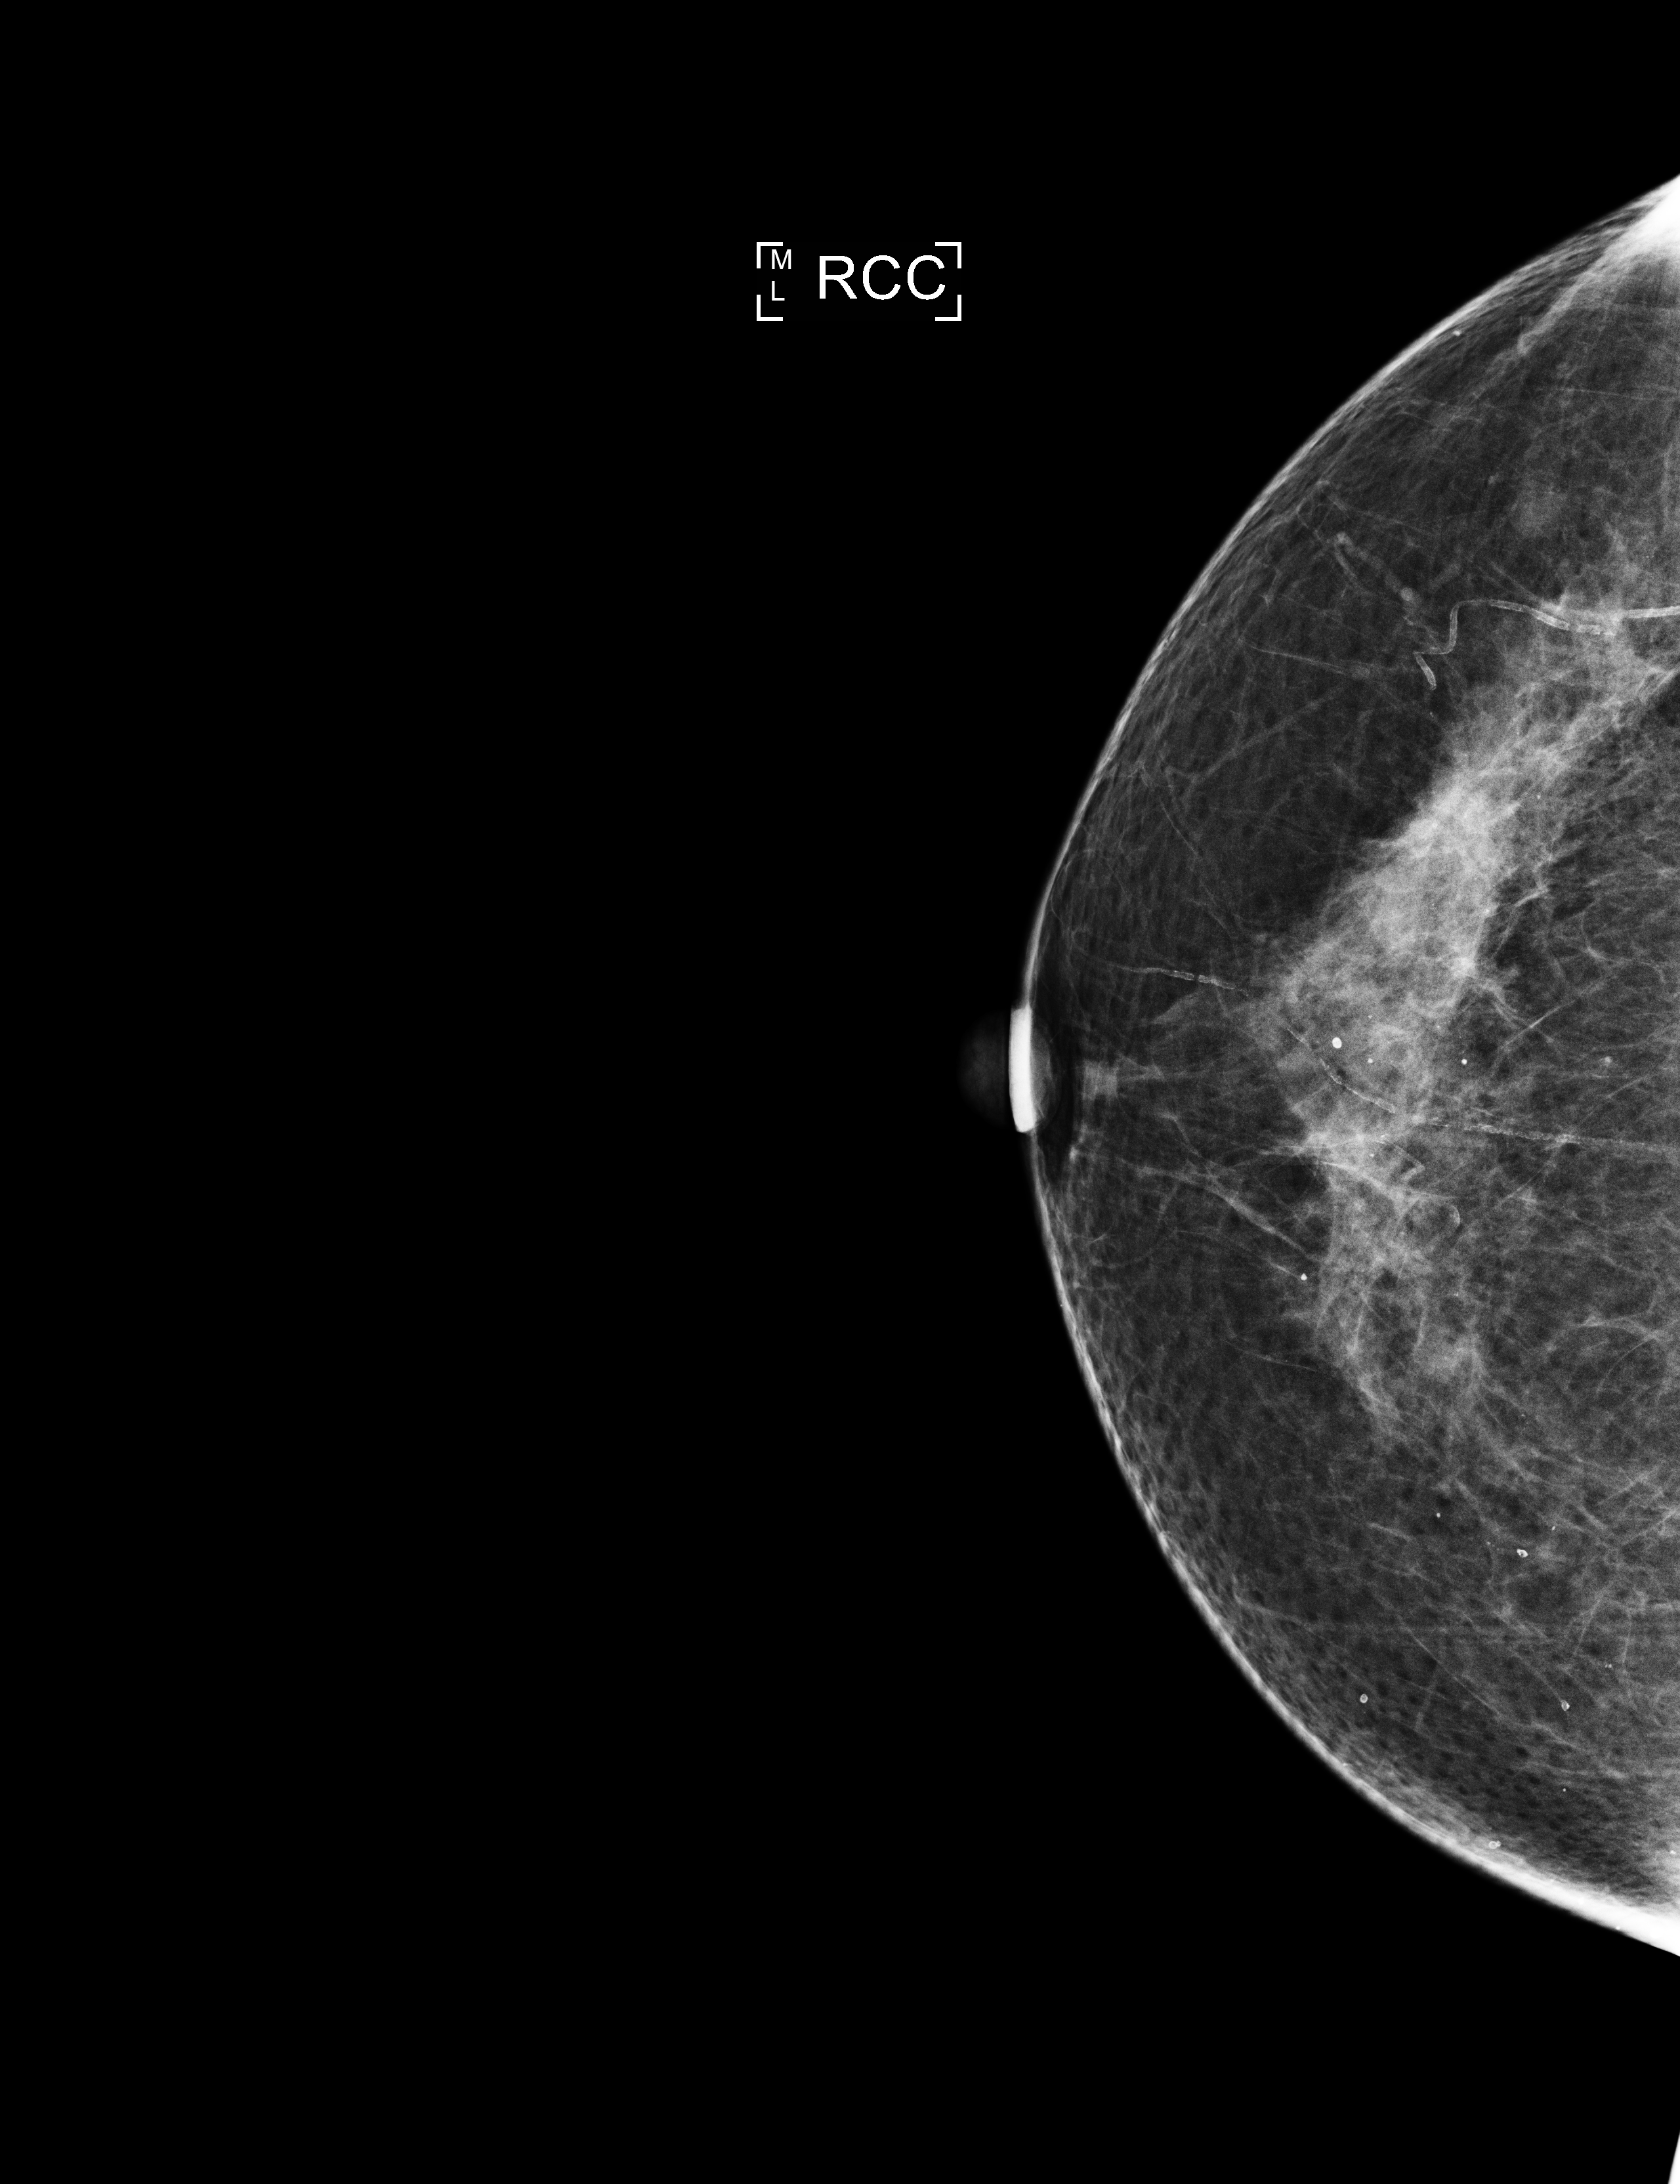
Annual screening mammography examination. Patient aged 68 years (female).
Image type: full-field digital mammogram. Breast: right. Projection: CC view. Breast density at the screening exam (both breasts): heterogeneously dense (BI-RADS density category c). Final BI-RADS category for the screening round (tomosynthesis exam, both breasts): category 2. Recall: no recall after this screen.